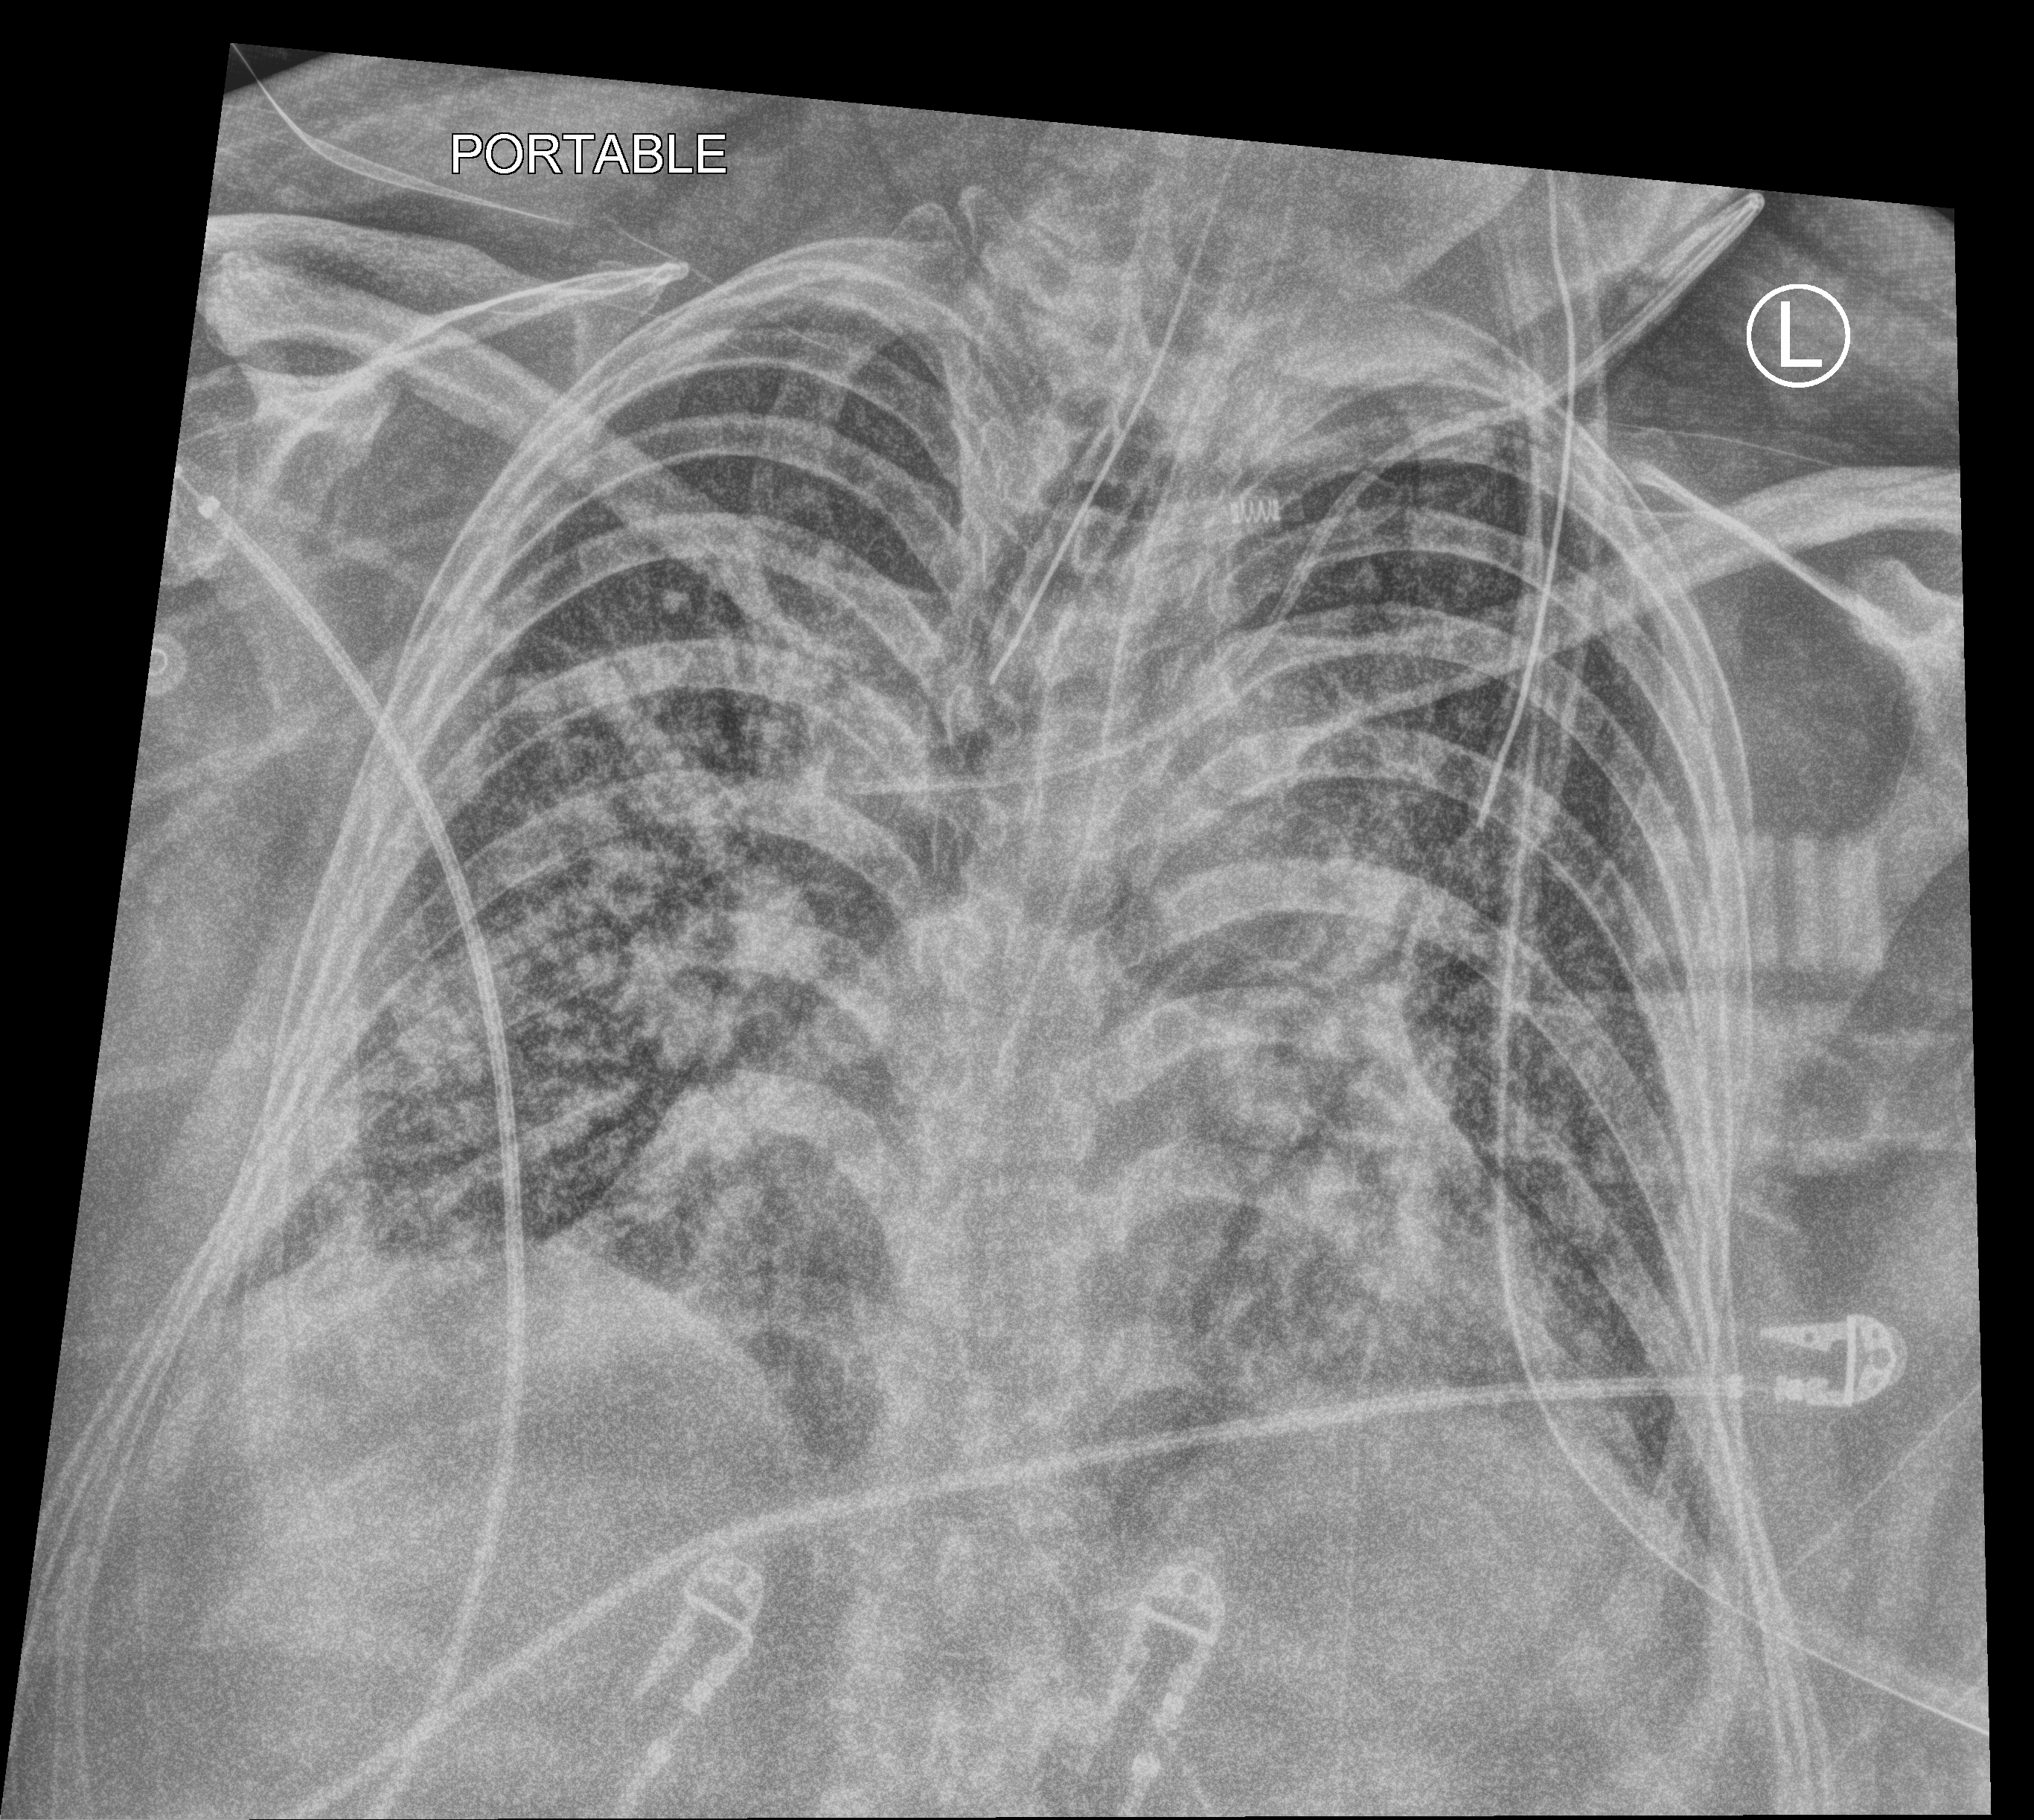
Portable chest radiograph. Adult patient hospitalised with COVID-19, age 18–59 years.
Admission-level facts for this patient (not findings on this image; timing relative to this image not recorded):
- smoking status (admission record): never
- diabetes (admission record): no